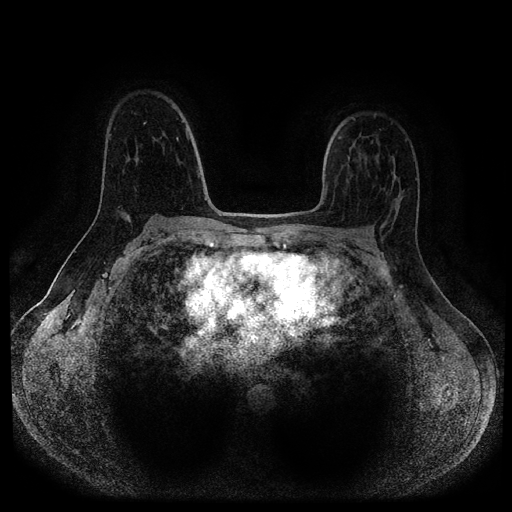
Breast MRI (dynamic contrast-enhanced, multi-phase), one axial slice; slice 69 of 116 in the series (ordered by position); dynamic contrast-enhanced series, time point 2 of 5 at this slice position (early post-contrast); 1.5 T; TE 2.7 ms, TR 5.4 ms; 512 × 512 image matrix, field of view 340 × 340 mm. Patient: female, 40 years.
Structures marked on this image (semi-automatic segmentation, software-assisted and operator-edited):
- breast lesion (labelled benign in the annotation): bounding box [x1, y1, x2, y2] px = [117, 208, 132, 223]